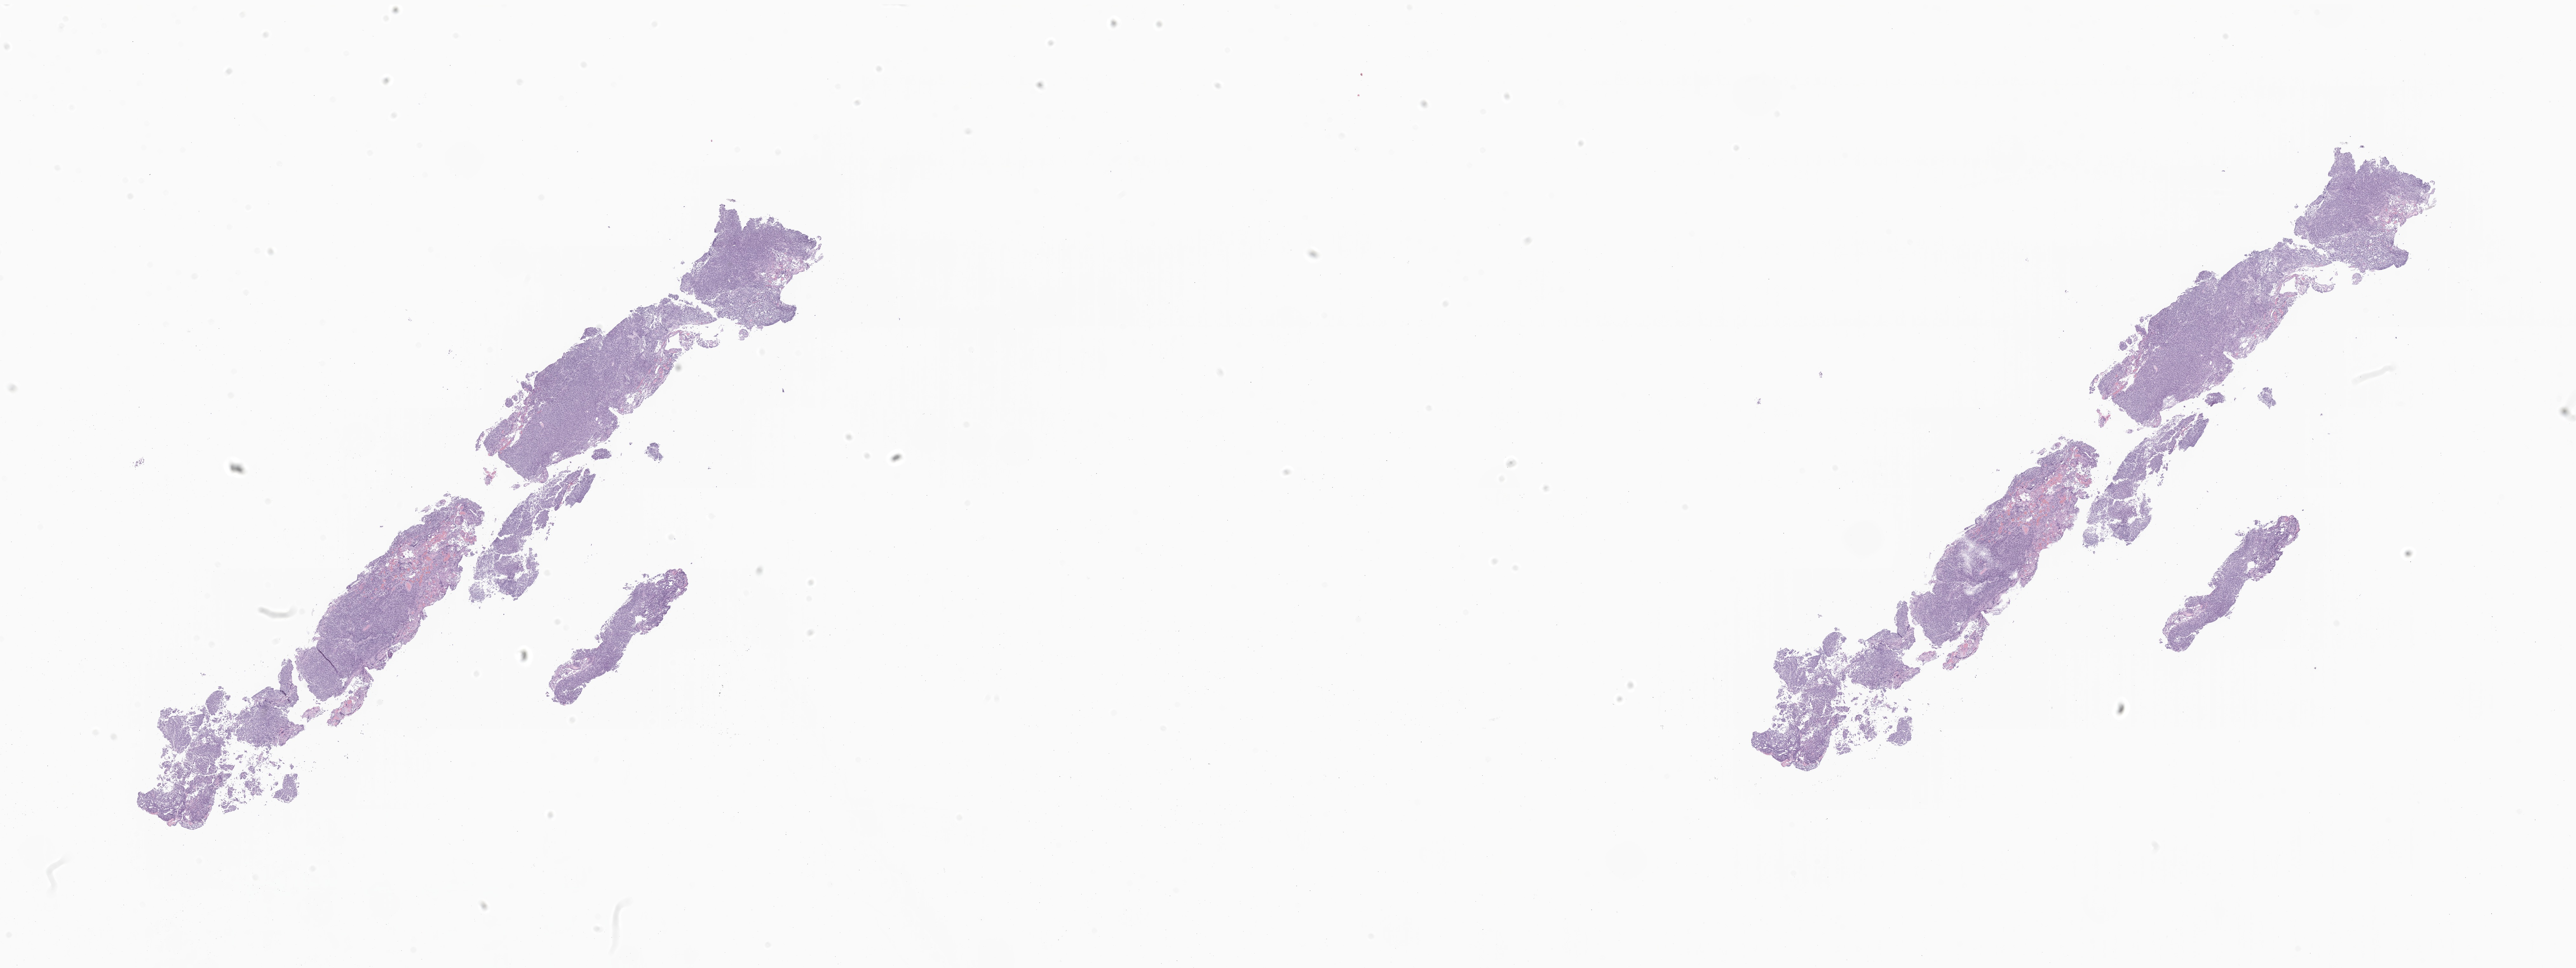
Haematoxylin and eosin whole-slide image of tumor tissue from the brain — low-resolution overview of the scanned area, about 34.2 x 12.8 mm; formalin-fixed paraffin-embedded section. Patient male; age 62 months (5 years 2 months).
* recorded diagnosis: Medulloblastoma, NOS